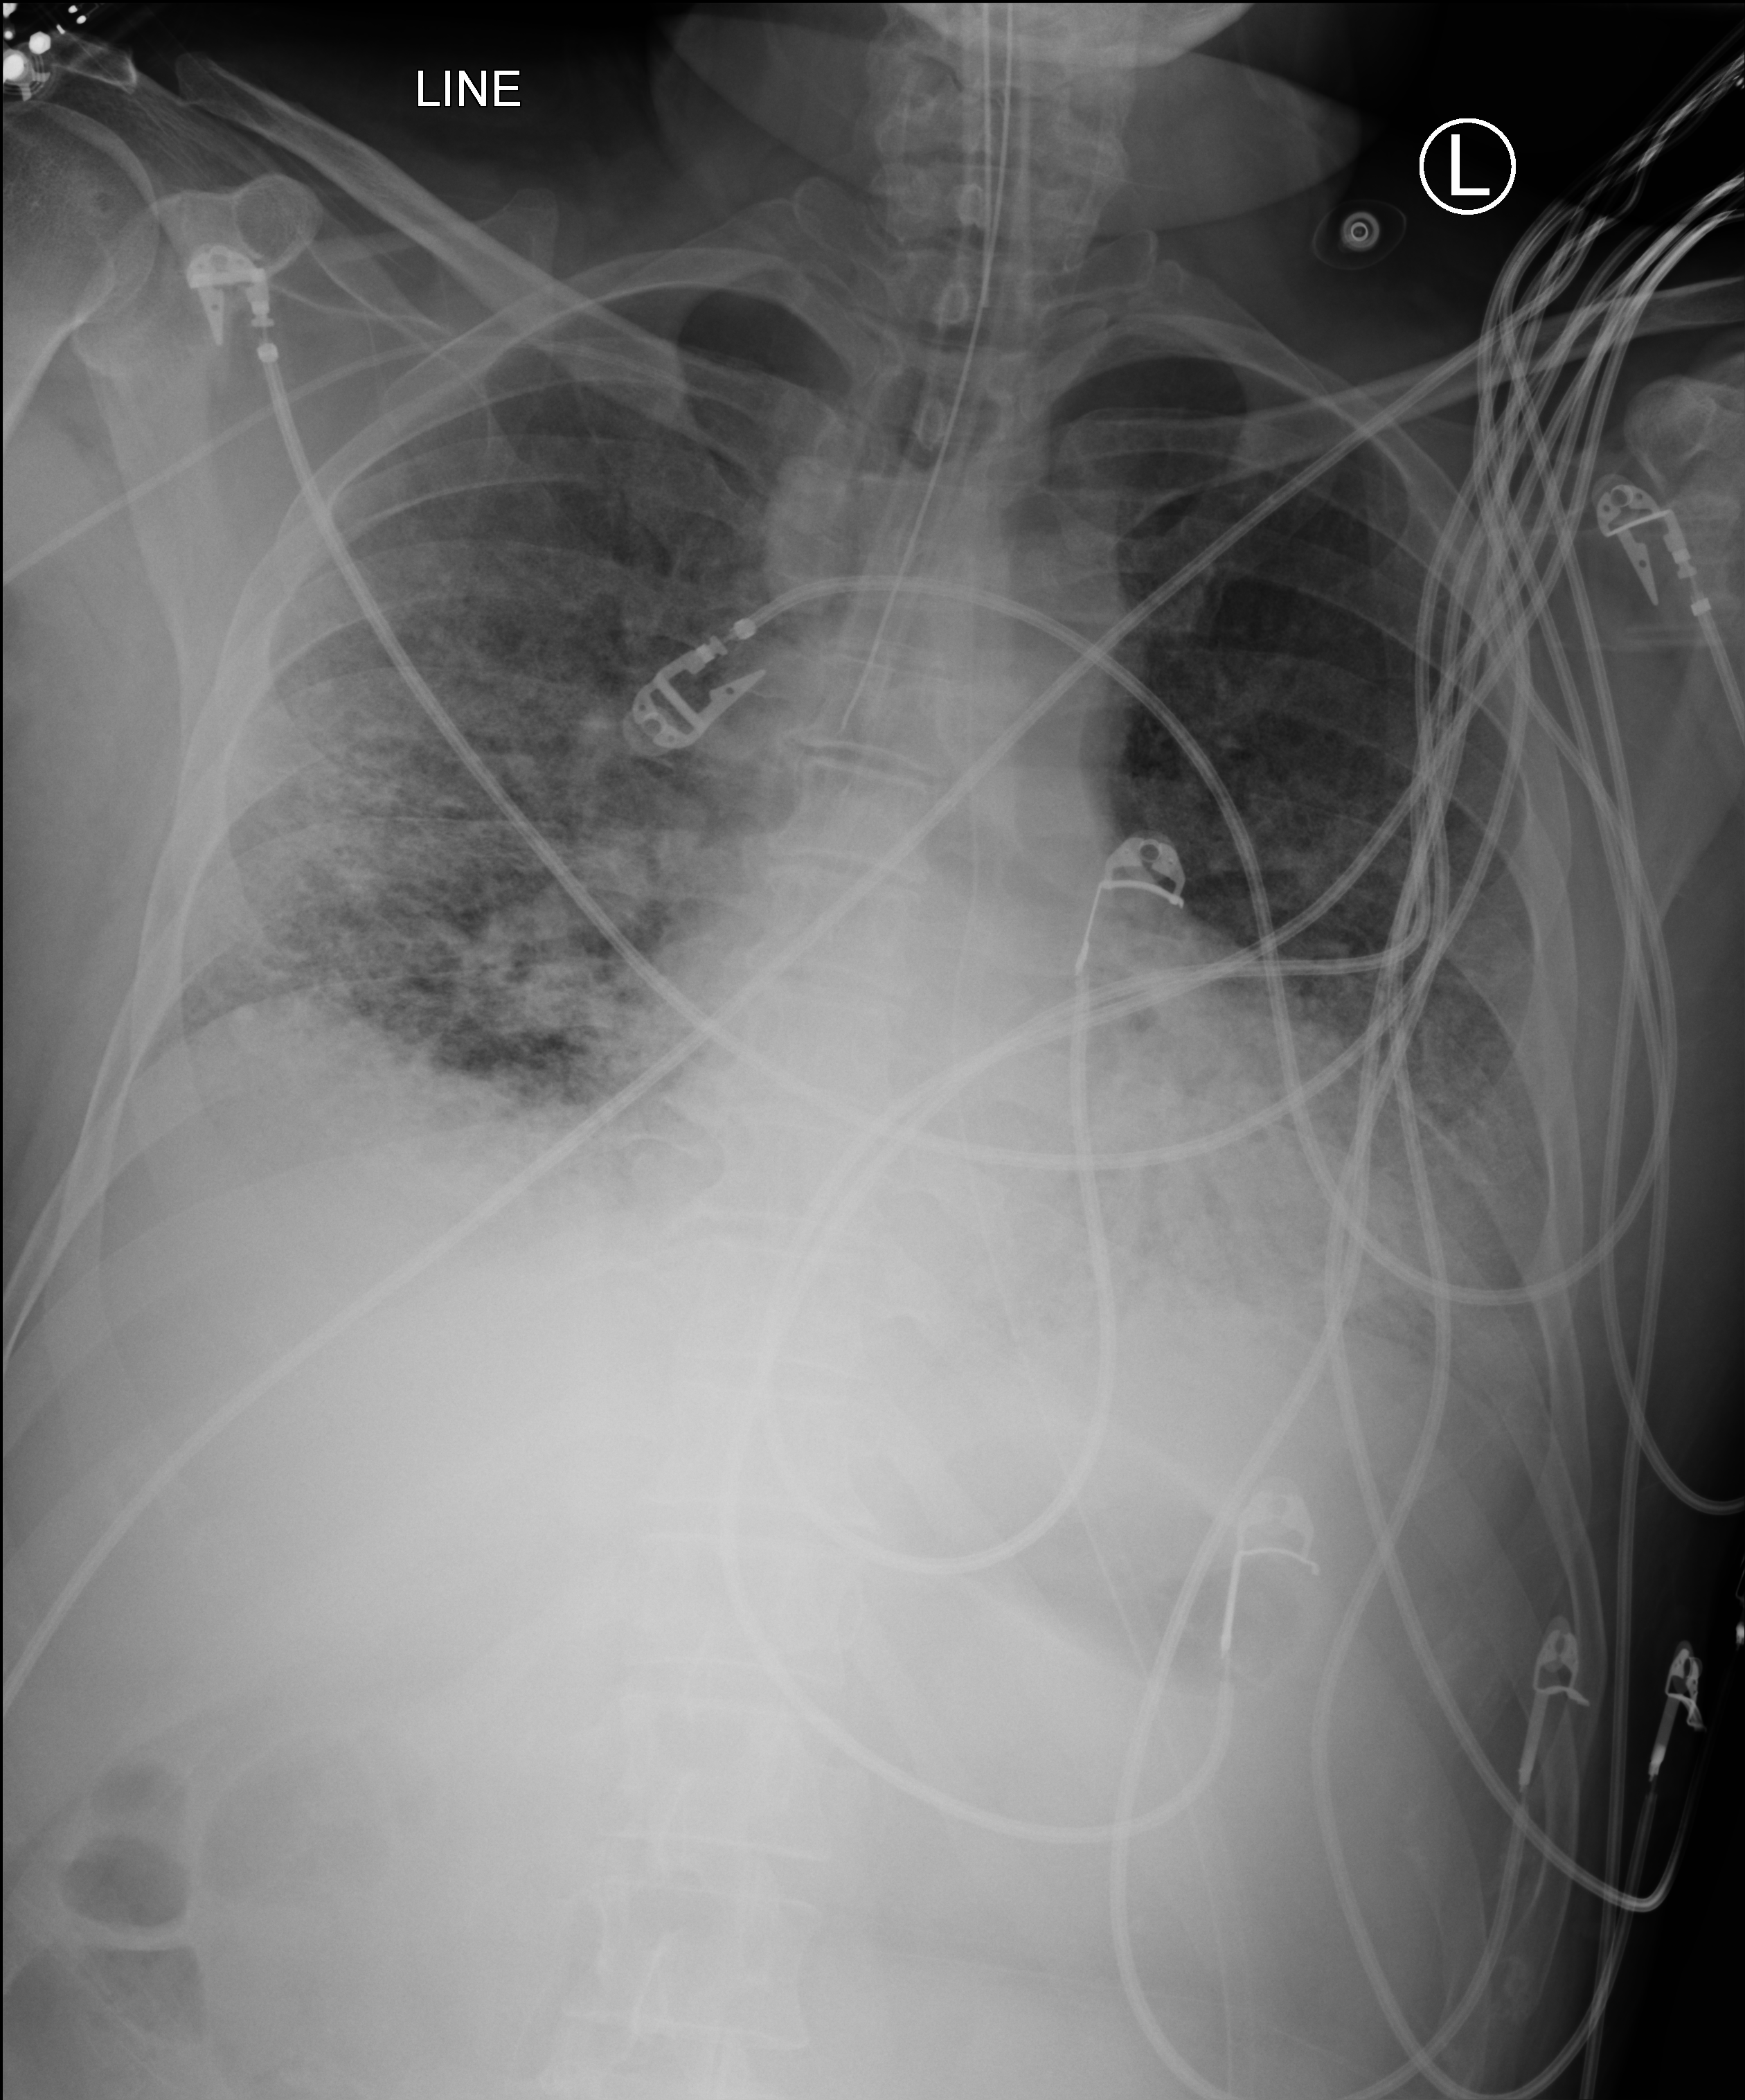
Portable chest radiograph, anteroposterior (AP) projection. Patient hospitalised with COVID-19; male, aged 18–59 years.
From the hospital-stay record, not from the radiograph (when in the stay this image was taken is not recorded): hypertension (admission record): no.